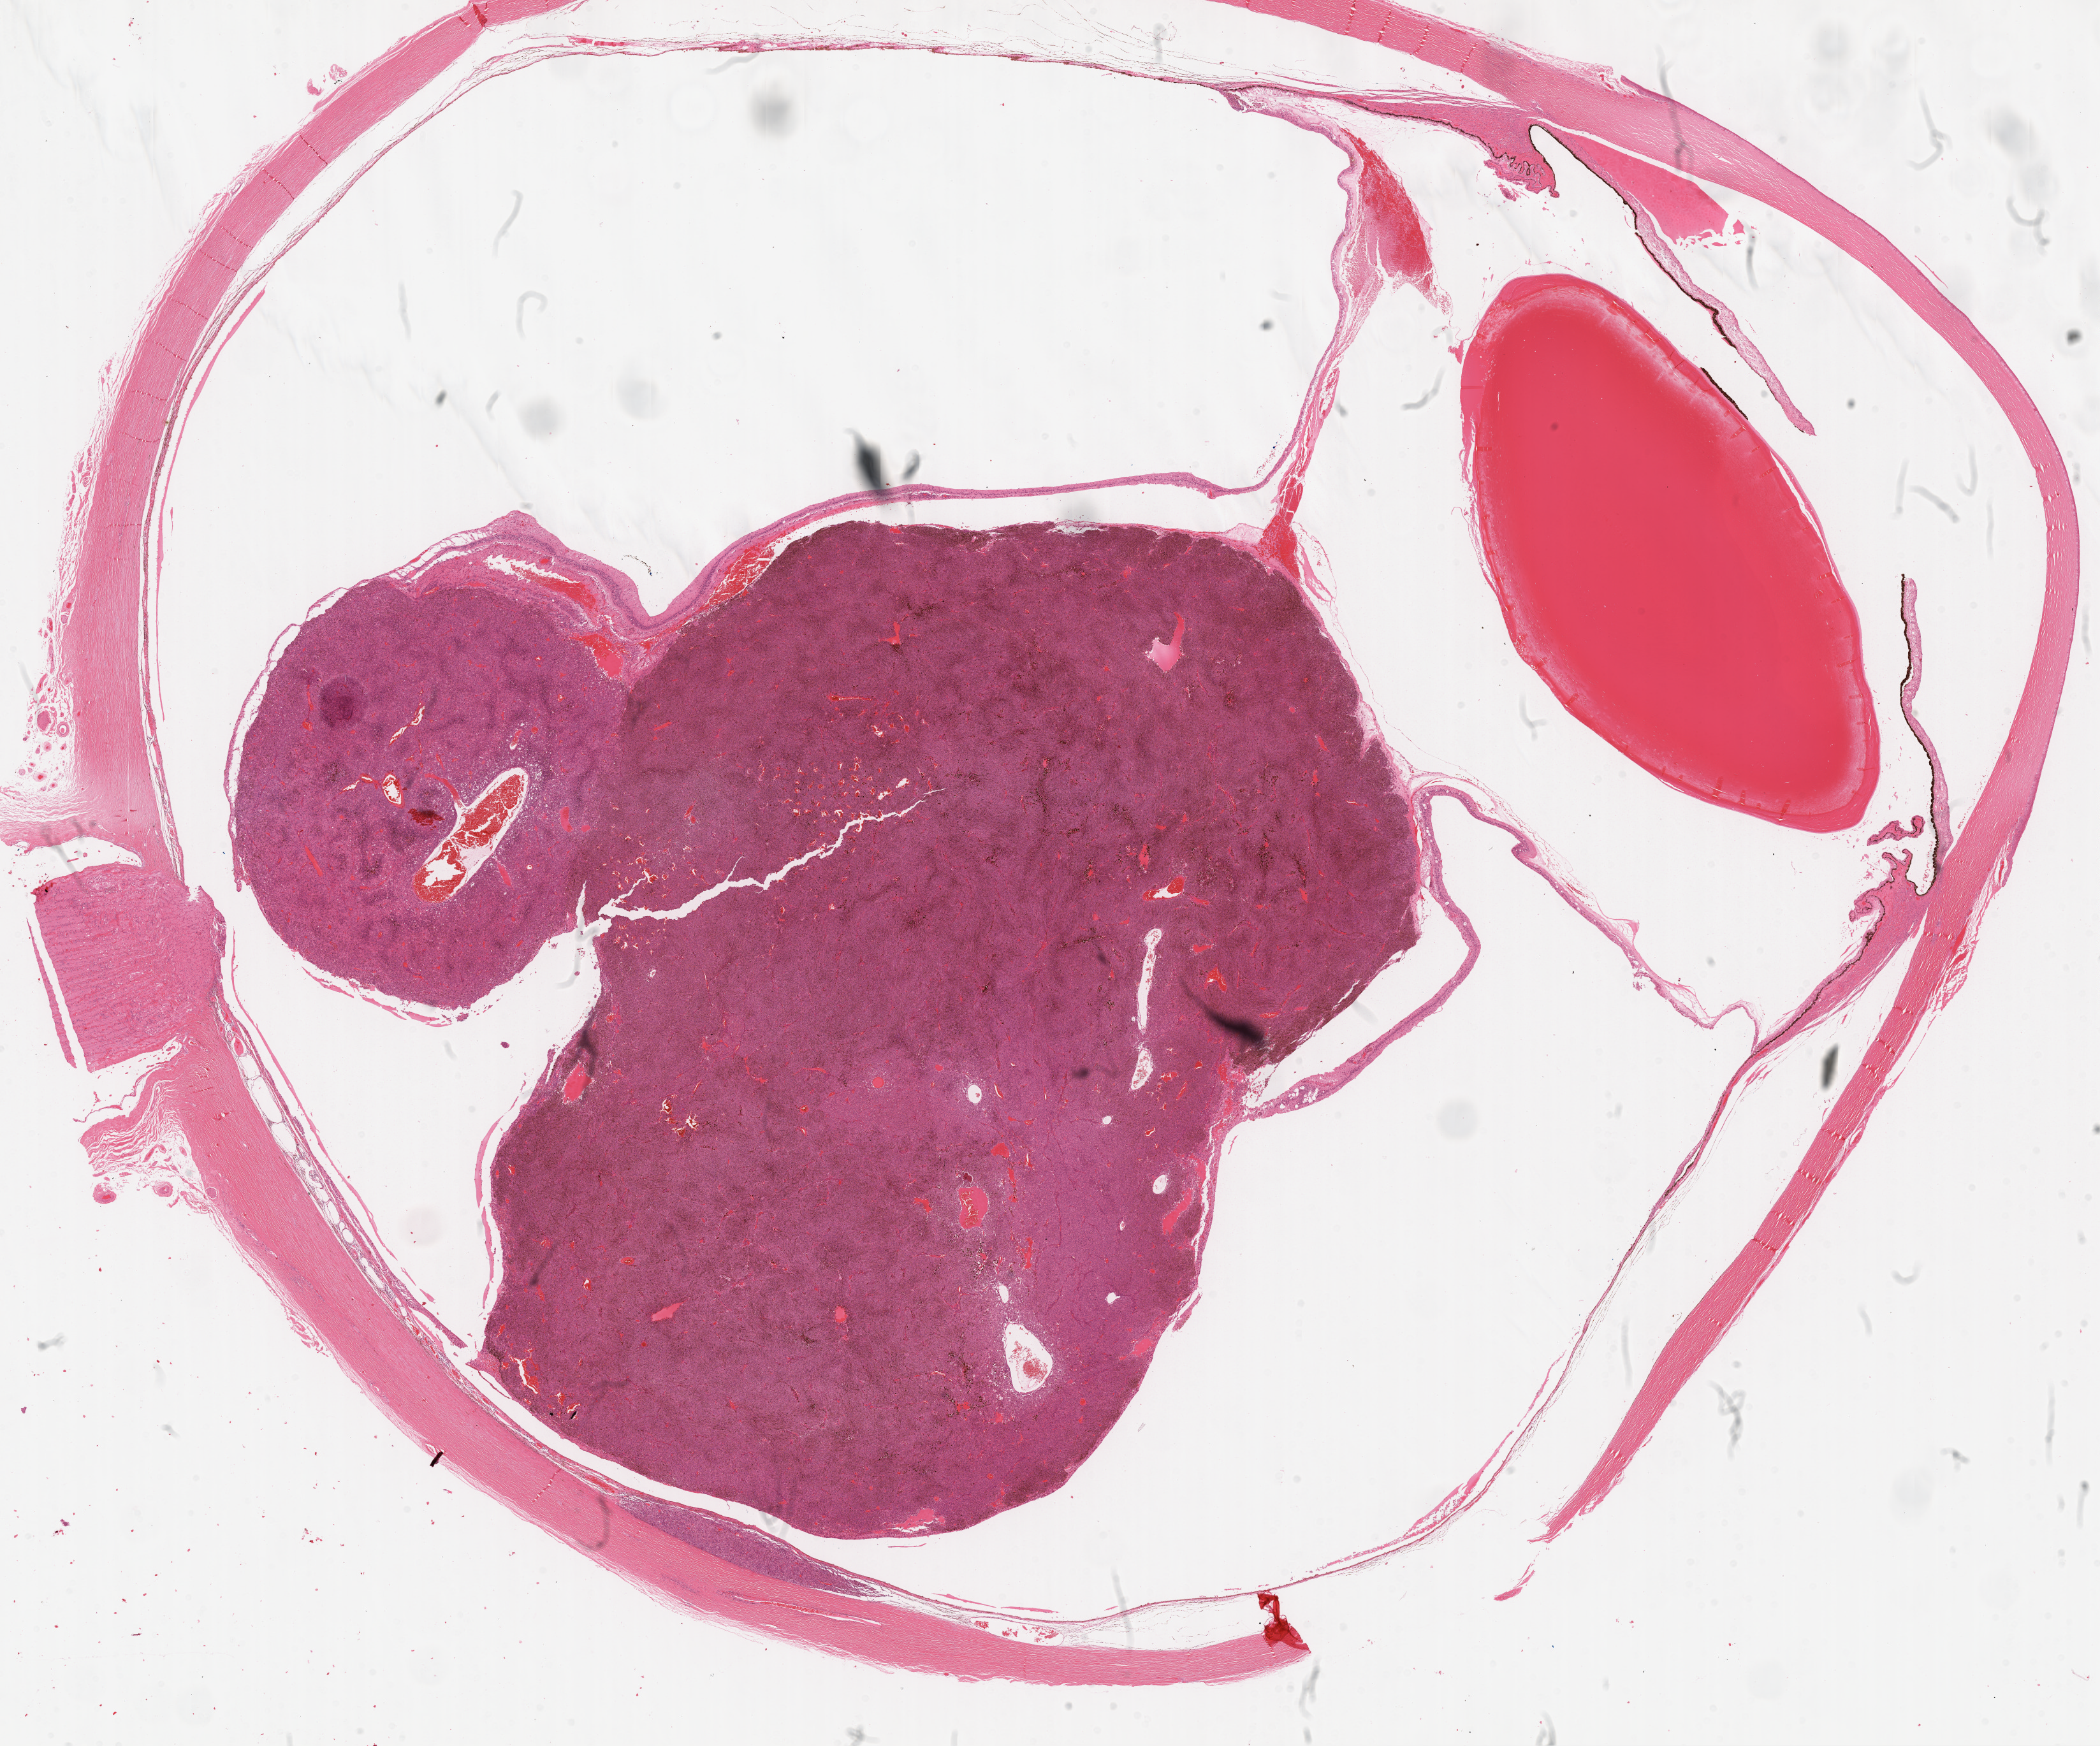
H&E-stained whole-slide image — a low-resolution overview of the entire scanned area, about 26.6 x 22.1 mm (from a 20x scan), formalin-fixed paraffin-embedded (FFPE) diagnostic section, uvea, primary tumour sample. Male, age 72 years at initial diagnosis.
Diagnosis: Mixed epithelioid and spindle cell melanoma (choroid).